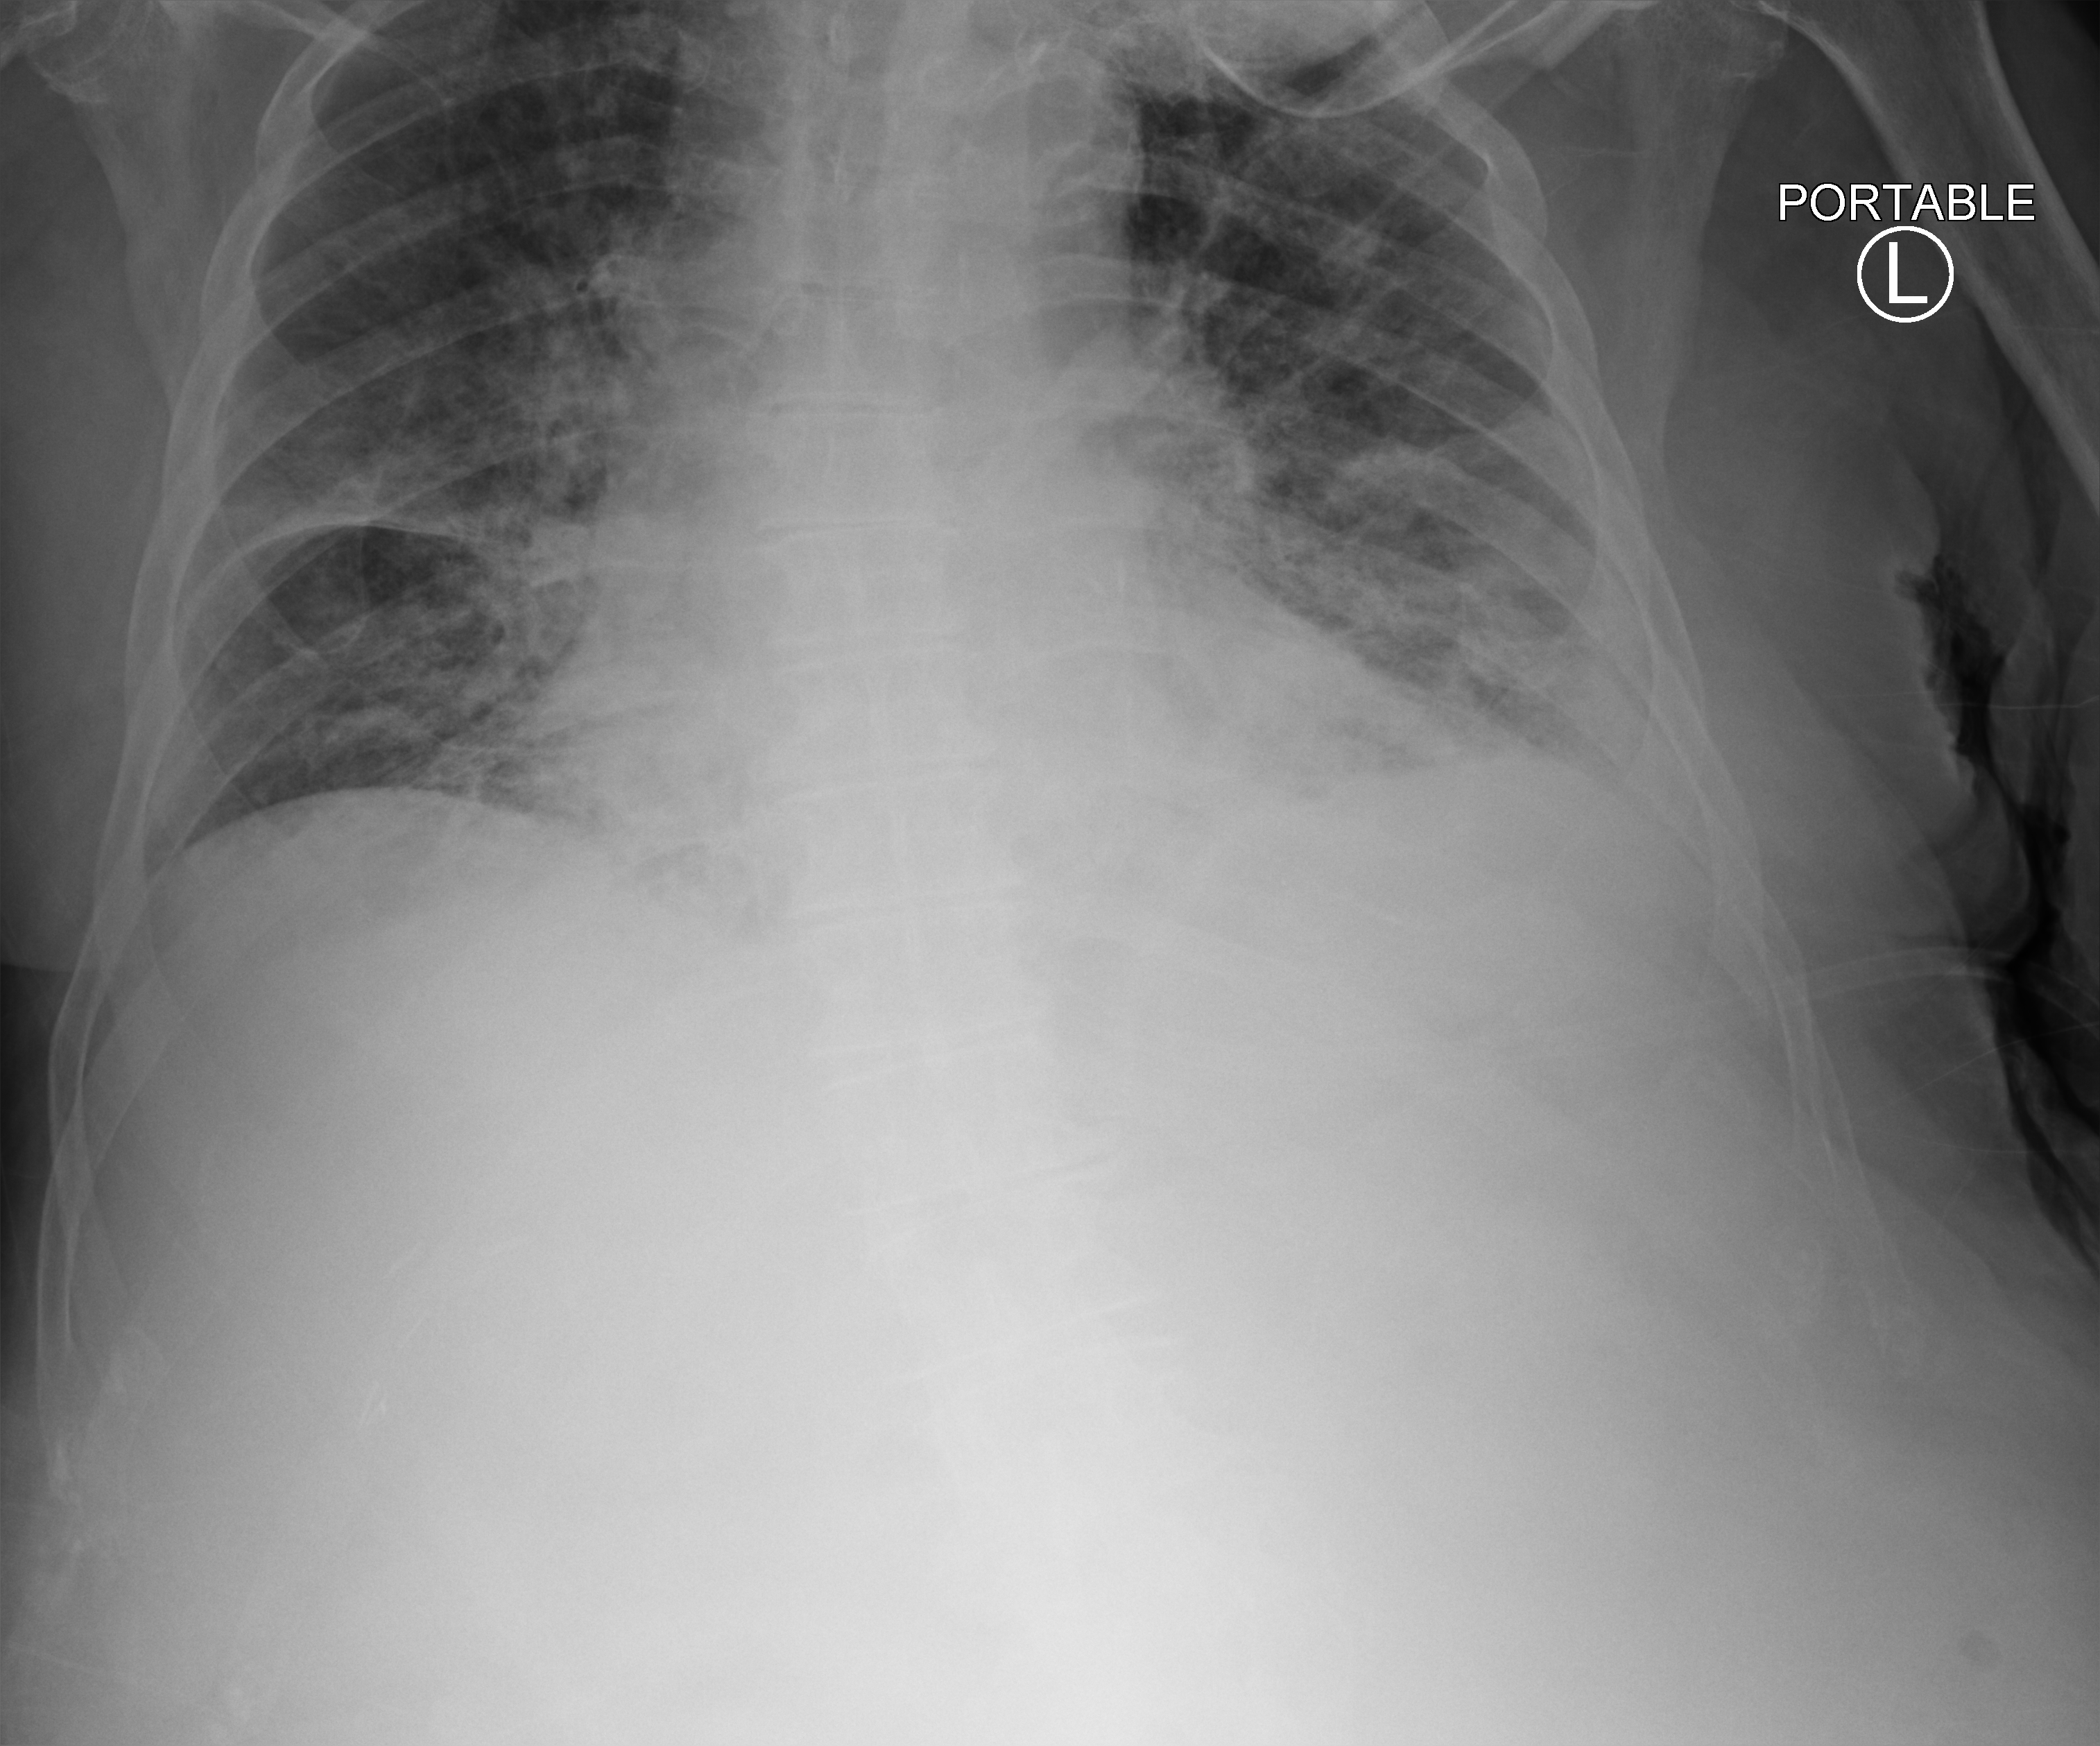
Chest X-ray (portable); anteroposterior (AP) projection. Male patient hospitalised with COVID-19, age 75–90 years.
Admission-level facts for this patient (not findings on this image; timing relative to this image not recorded): mechanically ventilated during this hospital stay: no; admitted to intensive care during this hospital stay: no.